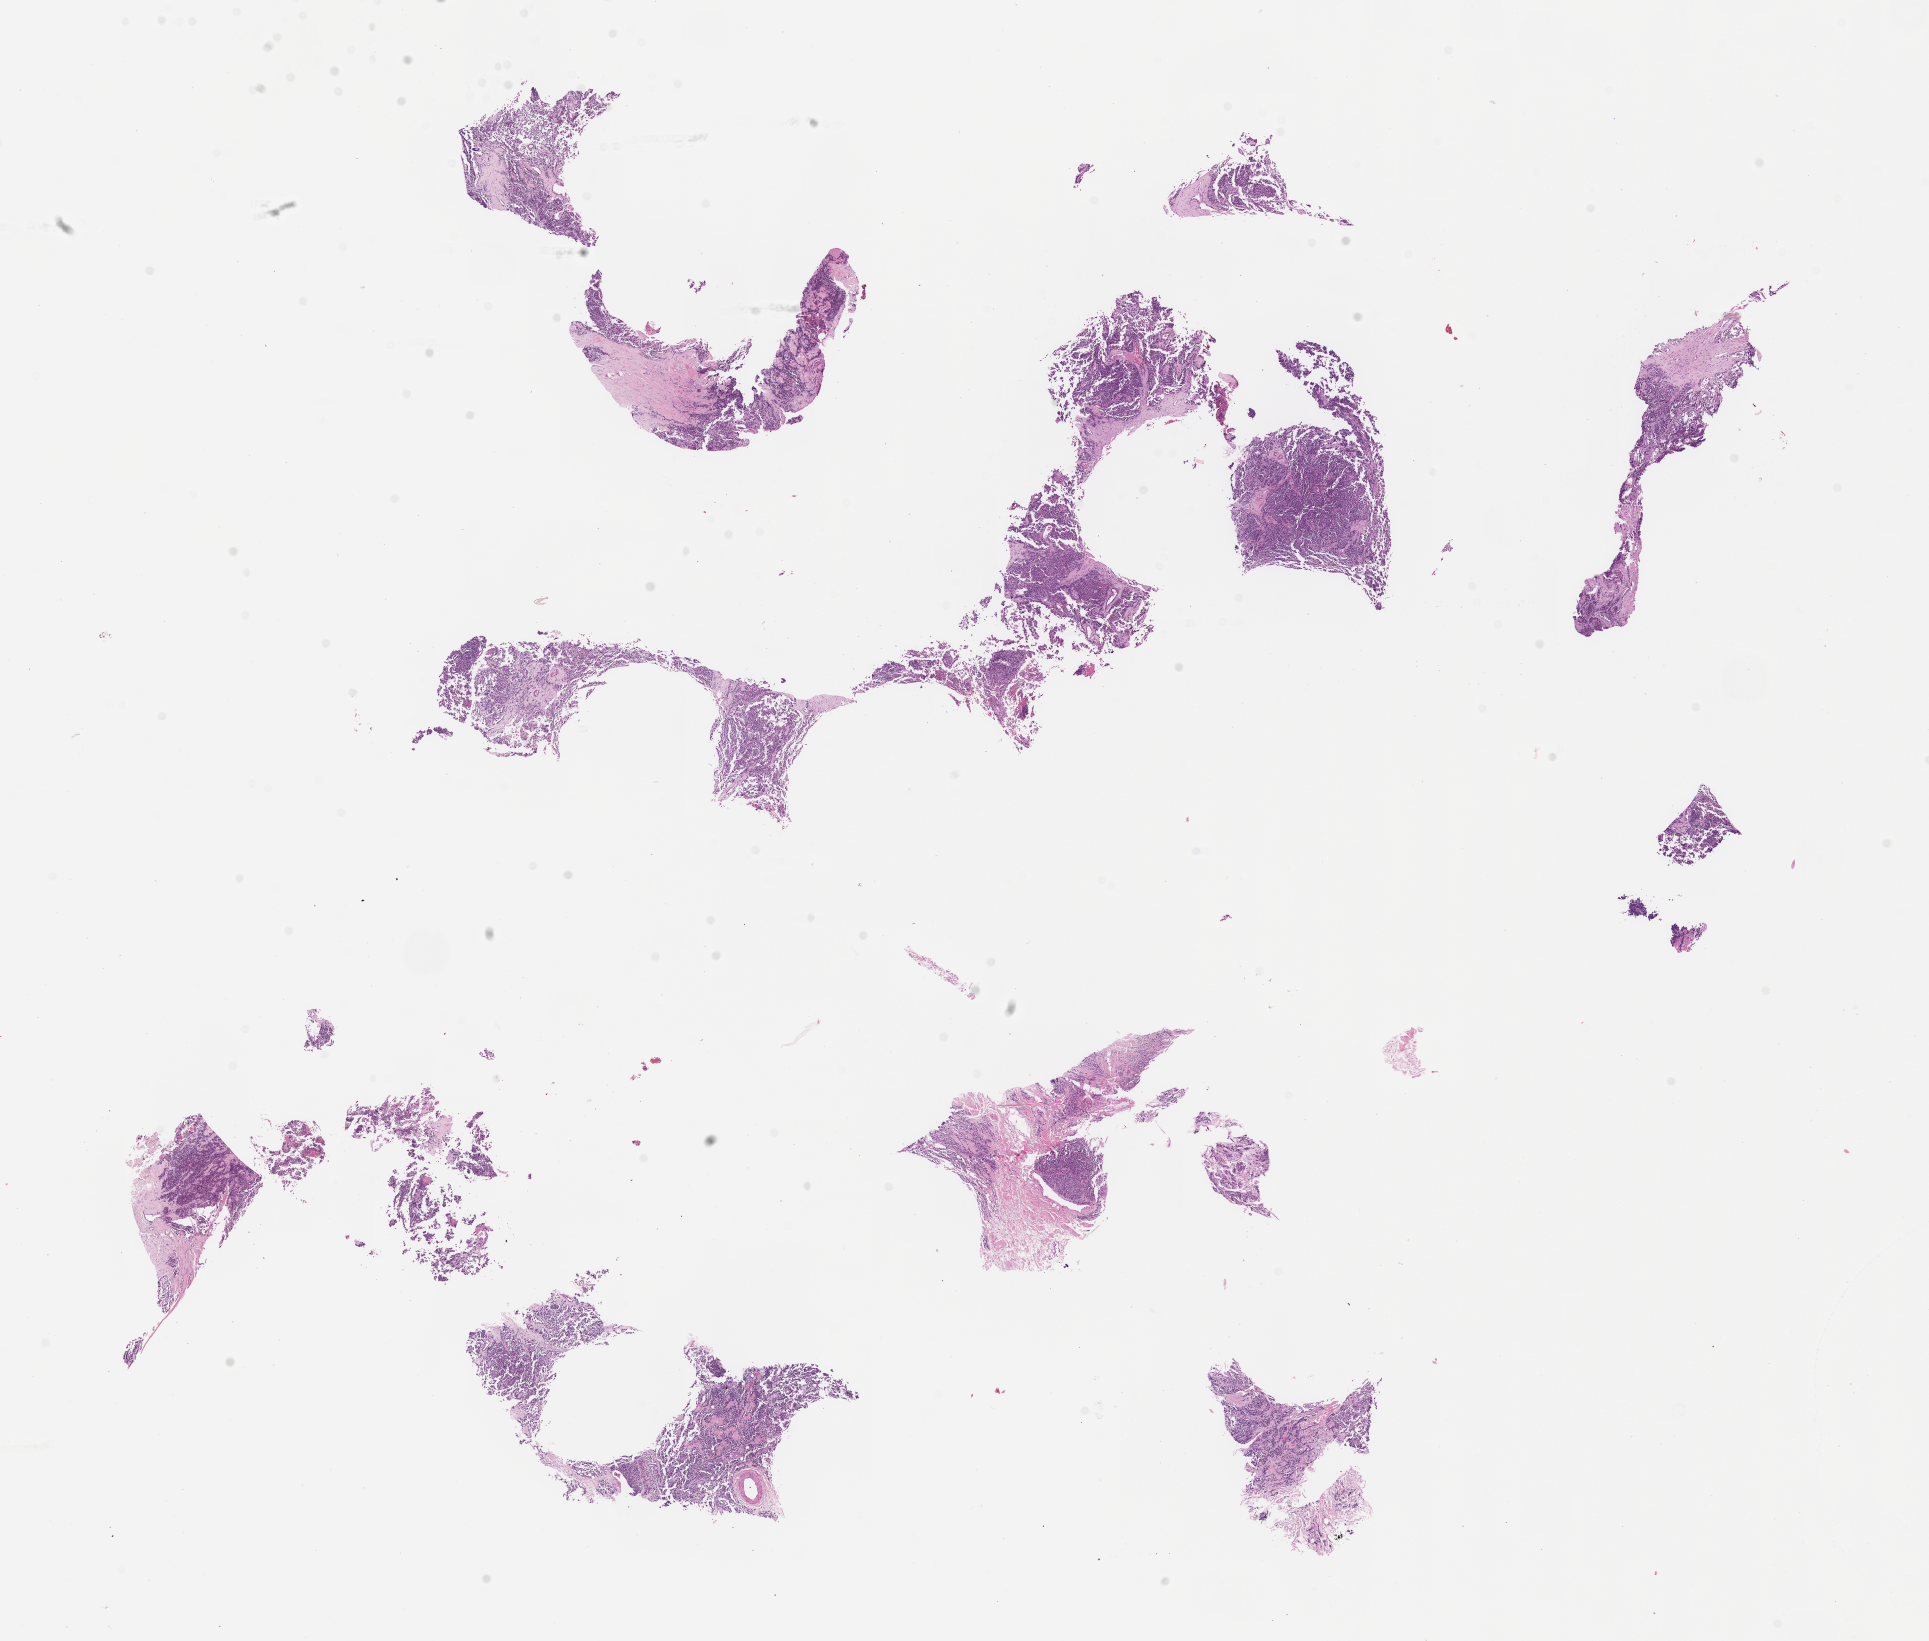
Hematoxylin and eosin (H&E) whole-slide image of tumor tissue, shown as a low-resolution overview of the whole scanned area (about 15.6 x 13.3 mm). FFPE section. Site: infratemporal, right. Patient: female, age 15.7 years at diagnosis.
* stage (as recorded): 2
* diagnosis: rhabdomyosarcoma; histological classification: alveolar rhabdomyosarcoma